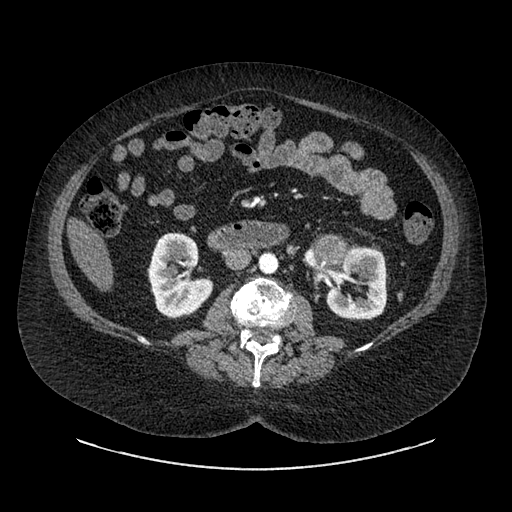
Contrast-enhanced abdominal CT, one axial slice. Slice 486 of 769 in the series (ordered by position). Reconstruction kernel SOFT. 120 kVp. Soft-tissue window (W 400 / L 40 HU). 0.62 mm slice thickness. 512 × 512 image matrix, field of view 460 × 460 mm. Female patient, age 61 years. Case-level facts recorded for this patient, not image findings: diagnosis: adrenocortical carcinoma; tumour side: left adrenal; tumour size at pathology: 13 cm; Ki-67 index: 79 %; stage (as recorded): 2.
Annotated regions visible in this slice (semi-automatic segmentation, software-assisted and operator-edited):
- mass: bounding box <323,242,340,263> (left, top, right, bottom; pixels)